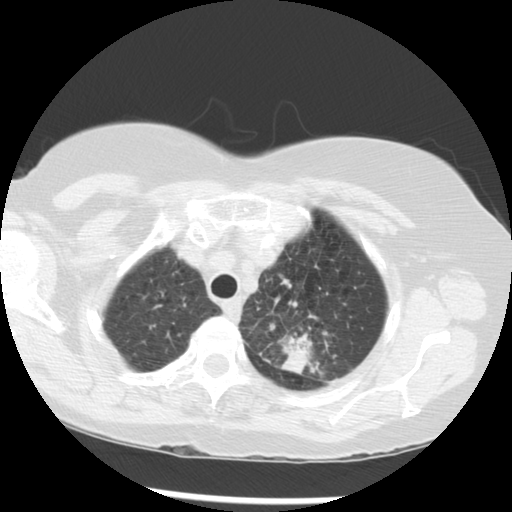
Chest CT (low-dose screening protocol), one axial image. Third screening round (two years after baseline). Lung window (W 1500 / L -600 HU). 2.5 mm slice thickness. Standard (soft-tissue) reconstruction kernel (STANDARD). Slice 239 of 283 in the series. Female, age 70 years at enrolment. Current smoker at enrolment.
• Lesion marked by an expert reader, bounding box <249,288,347,376> (left, top, right, bottom; pixels).
• The exam's reader record, not a measurement of the box and not confirmed to be the same lesion: non-calcified nodule or mass ≥4 mm, left upper lobe, 32 × 26 mm, spiculated (stellate) margins, soft tissue attenuation, pre-existing on the prior screen: yes; interval growth: yes.
• Official screen result: positive, other.
• Later outcome: lung cancer diagnosed 24 days after this screen — neoplasm, malignant, left upper lobe, stage IIIB (AJCC 6th edition), 40 mm at pathology.